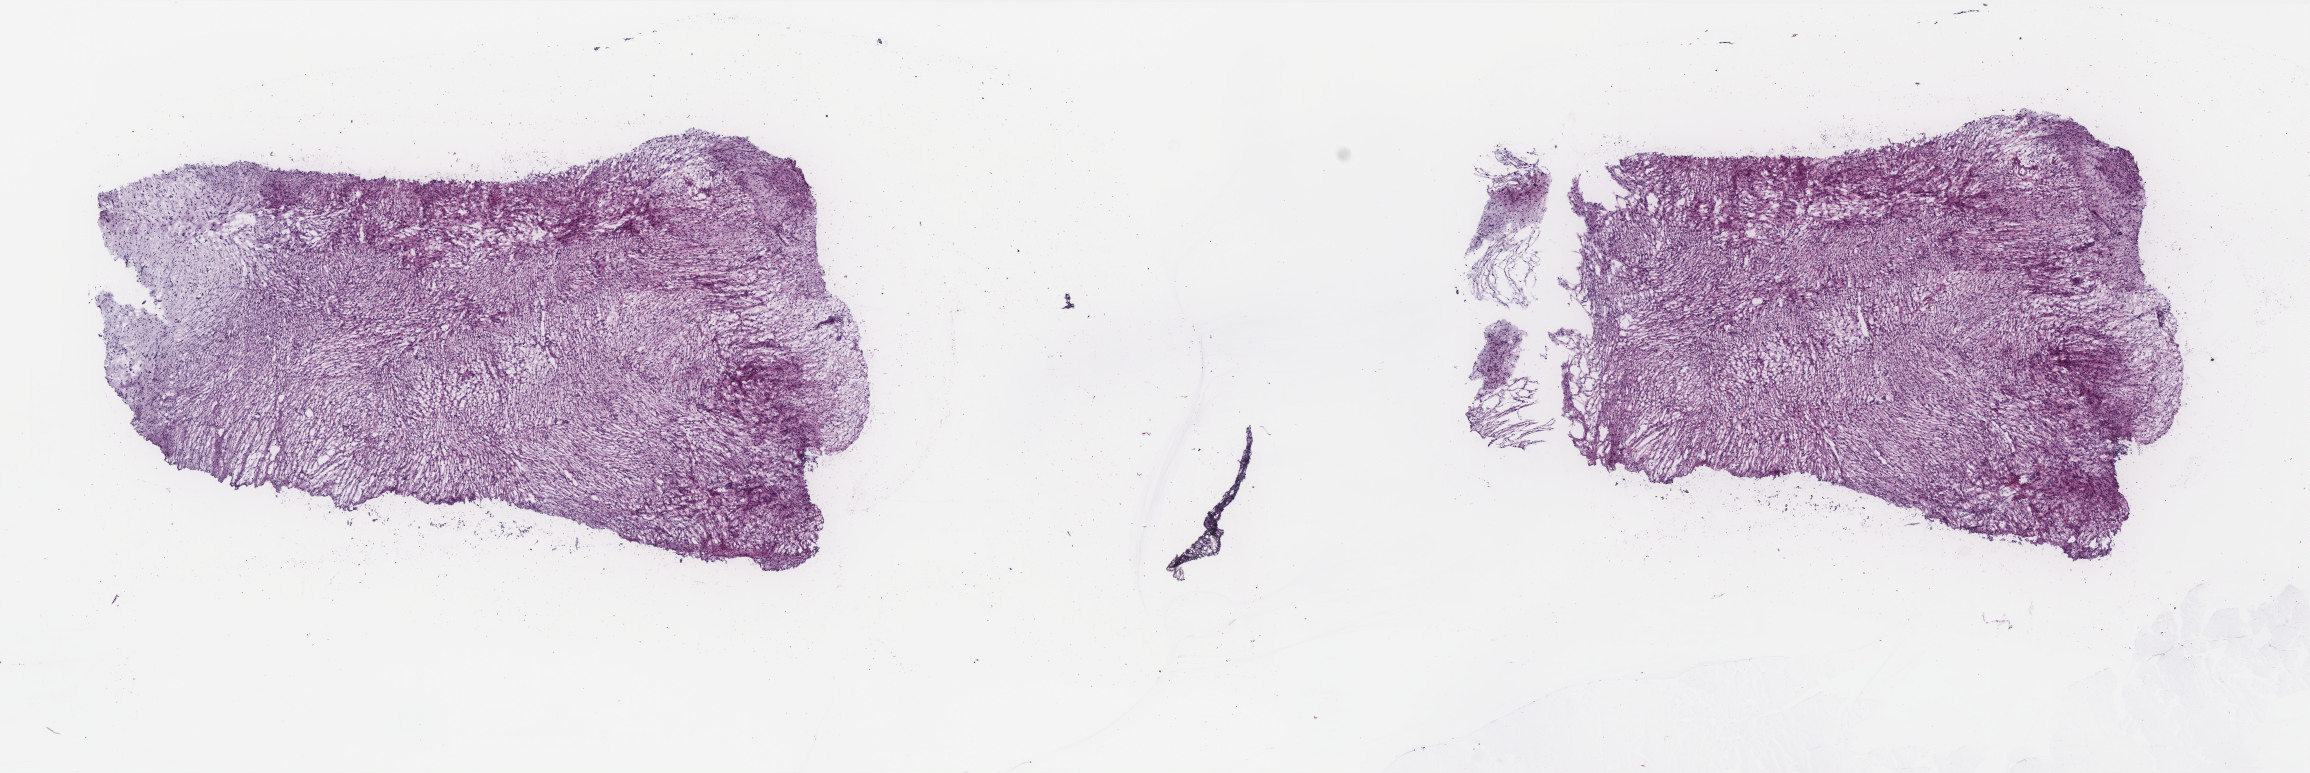
Digitized H&E tissue section (whole slide) — a low-resolution overview of the entire scanned area, about 18.5 x 6.2 mm (from a 40x scan). Frozen section from the top of the tissue portion. Primary tumour sample from the retroperitoneum and peritoneum. Male patient; age at initial diagnosis 58 years. Slide review estimates, as recorded: tumour cells 90%, tumour nuclei 90%, normal cells 0%, stromal cells 10%, necrosis 0%. Infiltration values recorded for this section: lymphocyte infiltration 2%, monocyte infiltration 1%, neutrophil infiltration 1%.
- pathologic diagnosis: Dedifferentiated liposarcoma (retroperitoneum)